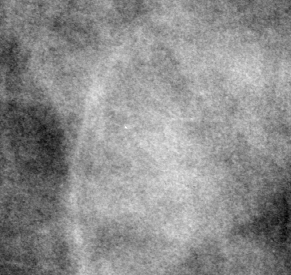
Crop from a digitized film mammogram around one marked abnormality, left breast, MLO view, BI-RADS breast density category 3 (scale 1–4).
Finding: mass, shape irregular, margins obscured / ill defined; BI-RADS assessment category 3; pathology result (as recorded, not read from the image): malignant.